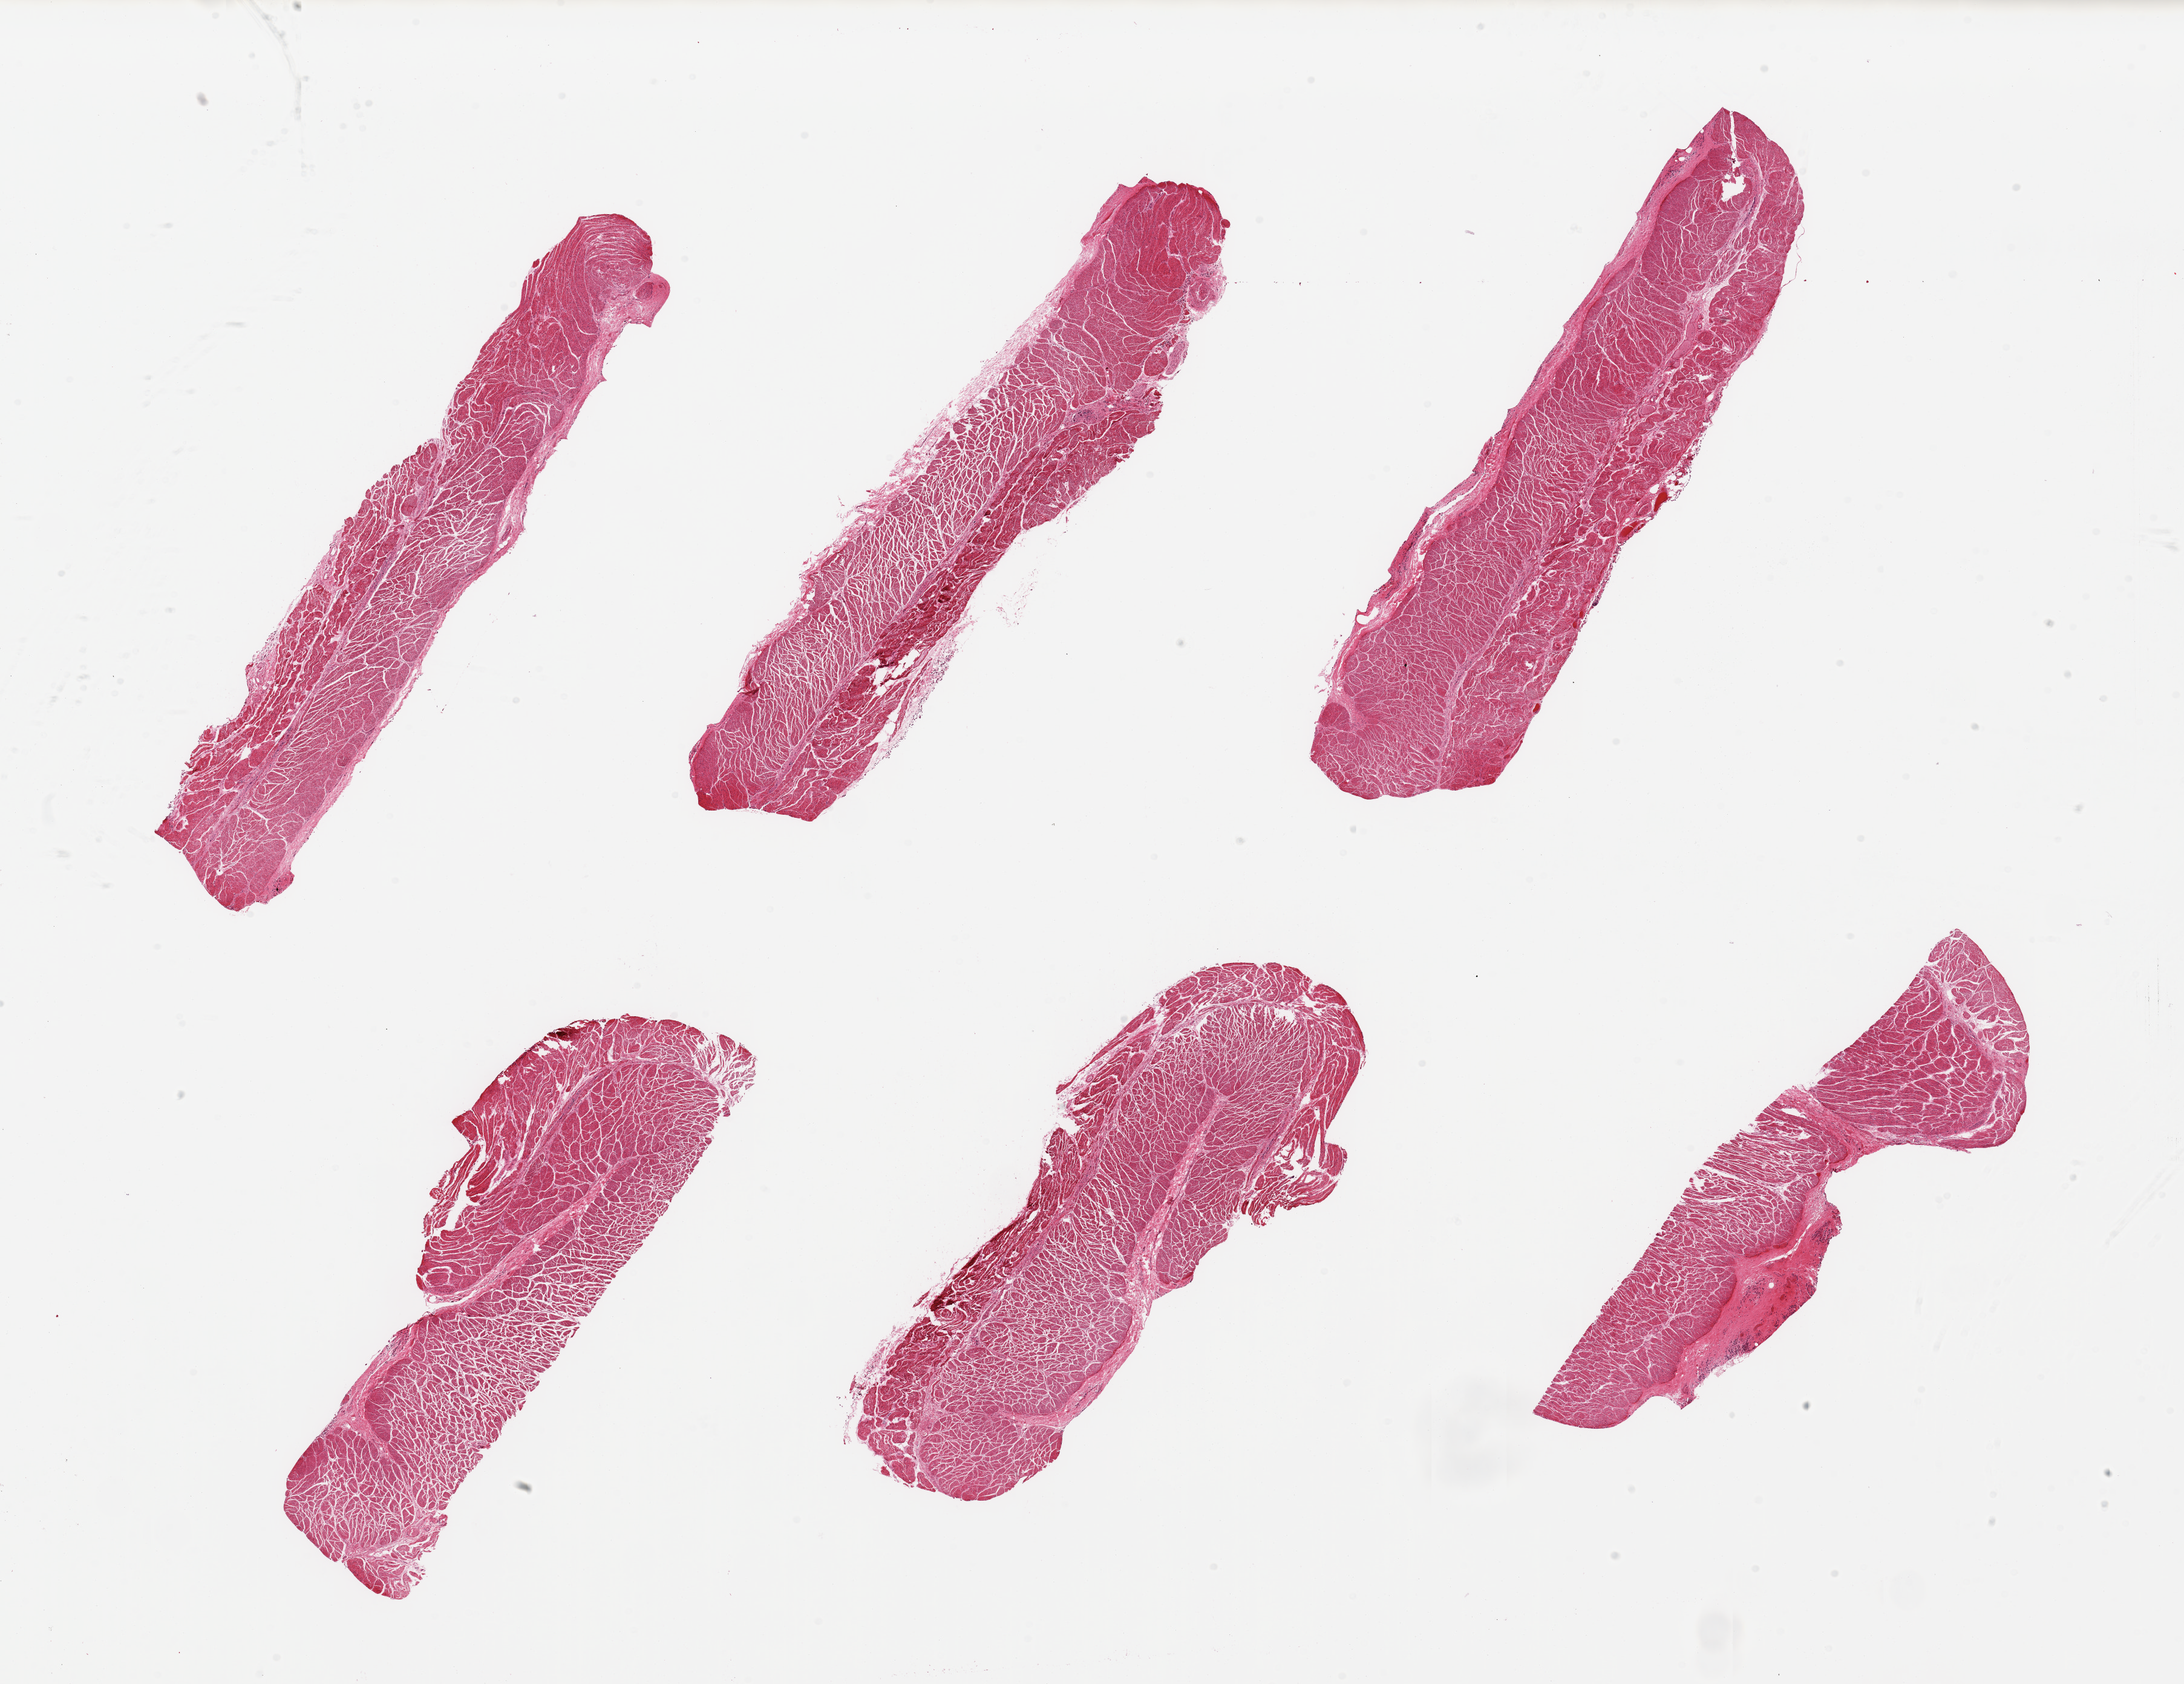
Whole-slide image, haematoxylin and eosin stain — a low-resolution overview of the entire scanned area, about 28.5 x 22.0 mm (slide scanned at 20x); PAXgene-fixed paraffin-embedded (PFPE) section; target tissue: esophageal muscle; donor tissue sample.
• review note (as recorded): 6 pieces; well dissected generally